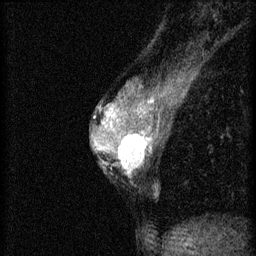
Breast MRI (dynamic contrast-enhanced), one sagittal slice. Slice 30 of 46 in the series (ordered by position). 3 images stored at this slice position (order not interpretable as contrast timing). 1.5 T. TE 4.2 ms, TR 8.2 ms. 2 mm slice thickness. 256 × 256 image matrix, field of view 180 × 180 mm. Female patient, age 44 years.
Outlined on this slice (semi-automatically segmented with operator editing):
- analysis volume of interest (the breast-tissue region the enhancement analysis was run in; not a lesion): bounding box <110,128,156,179> (left, top, right, bottom; pixels)
- tumour enhancement mask (voxels above the 70 % enhancement threshold inside the analysis volume of interest): <114,130,154,175>